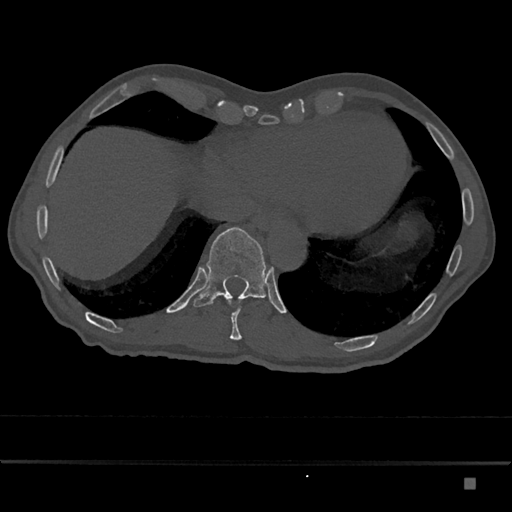
CT including the spine, one axial slice. Position 702 of 797 along the scan axis. Bone window (W 1800 / L 400 HU). 0.5 mm slice thickness. 512 × 512 image matrix, field of view 390 × 390 mm. Patient: male, 72 years. From the clinical record (not read from this slice): primary cancer: prostate.
Structures marked on this image (semi-automatically segmented with operator editing):
- T10 vertebra: bounding box <226,298,242,340> (left, top, right, bottom; pixels)
- T11 vertebra: <193,227,267,307>